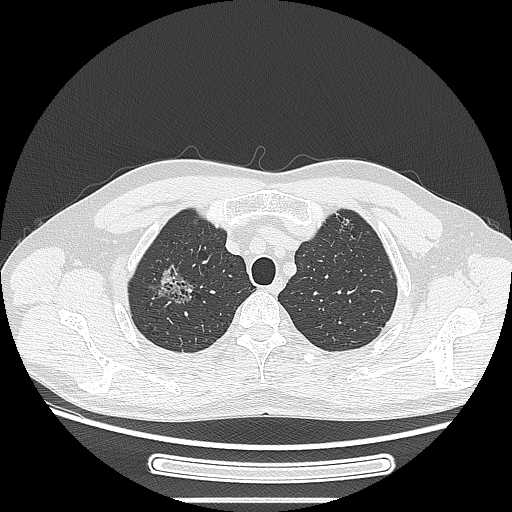
Chest CT, one axial slice. Reconstruction kernel LUNG. 120 kVp. Lung window (W 1500 / L -600 HU). 1.25 mm slice thickness. 512 × 512 image matrix, field of view 382 × 382 mm. Male patient, age 53 years. From the clinical record (not read from this slice): clinical TNM (as recorded): T1c N0 M0; histopathological grade: G2.
Outlined on this slice (bounding box drawn by a radiologist):
- lung tumour (recorded histology: adenocarcinoma): bounding box <148,256,195,311> (left, top, right, bottom; pixels)